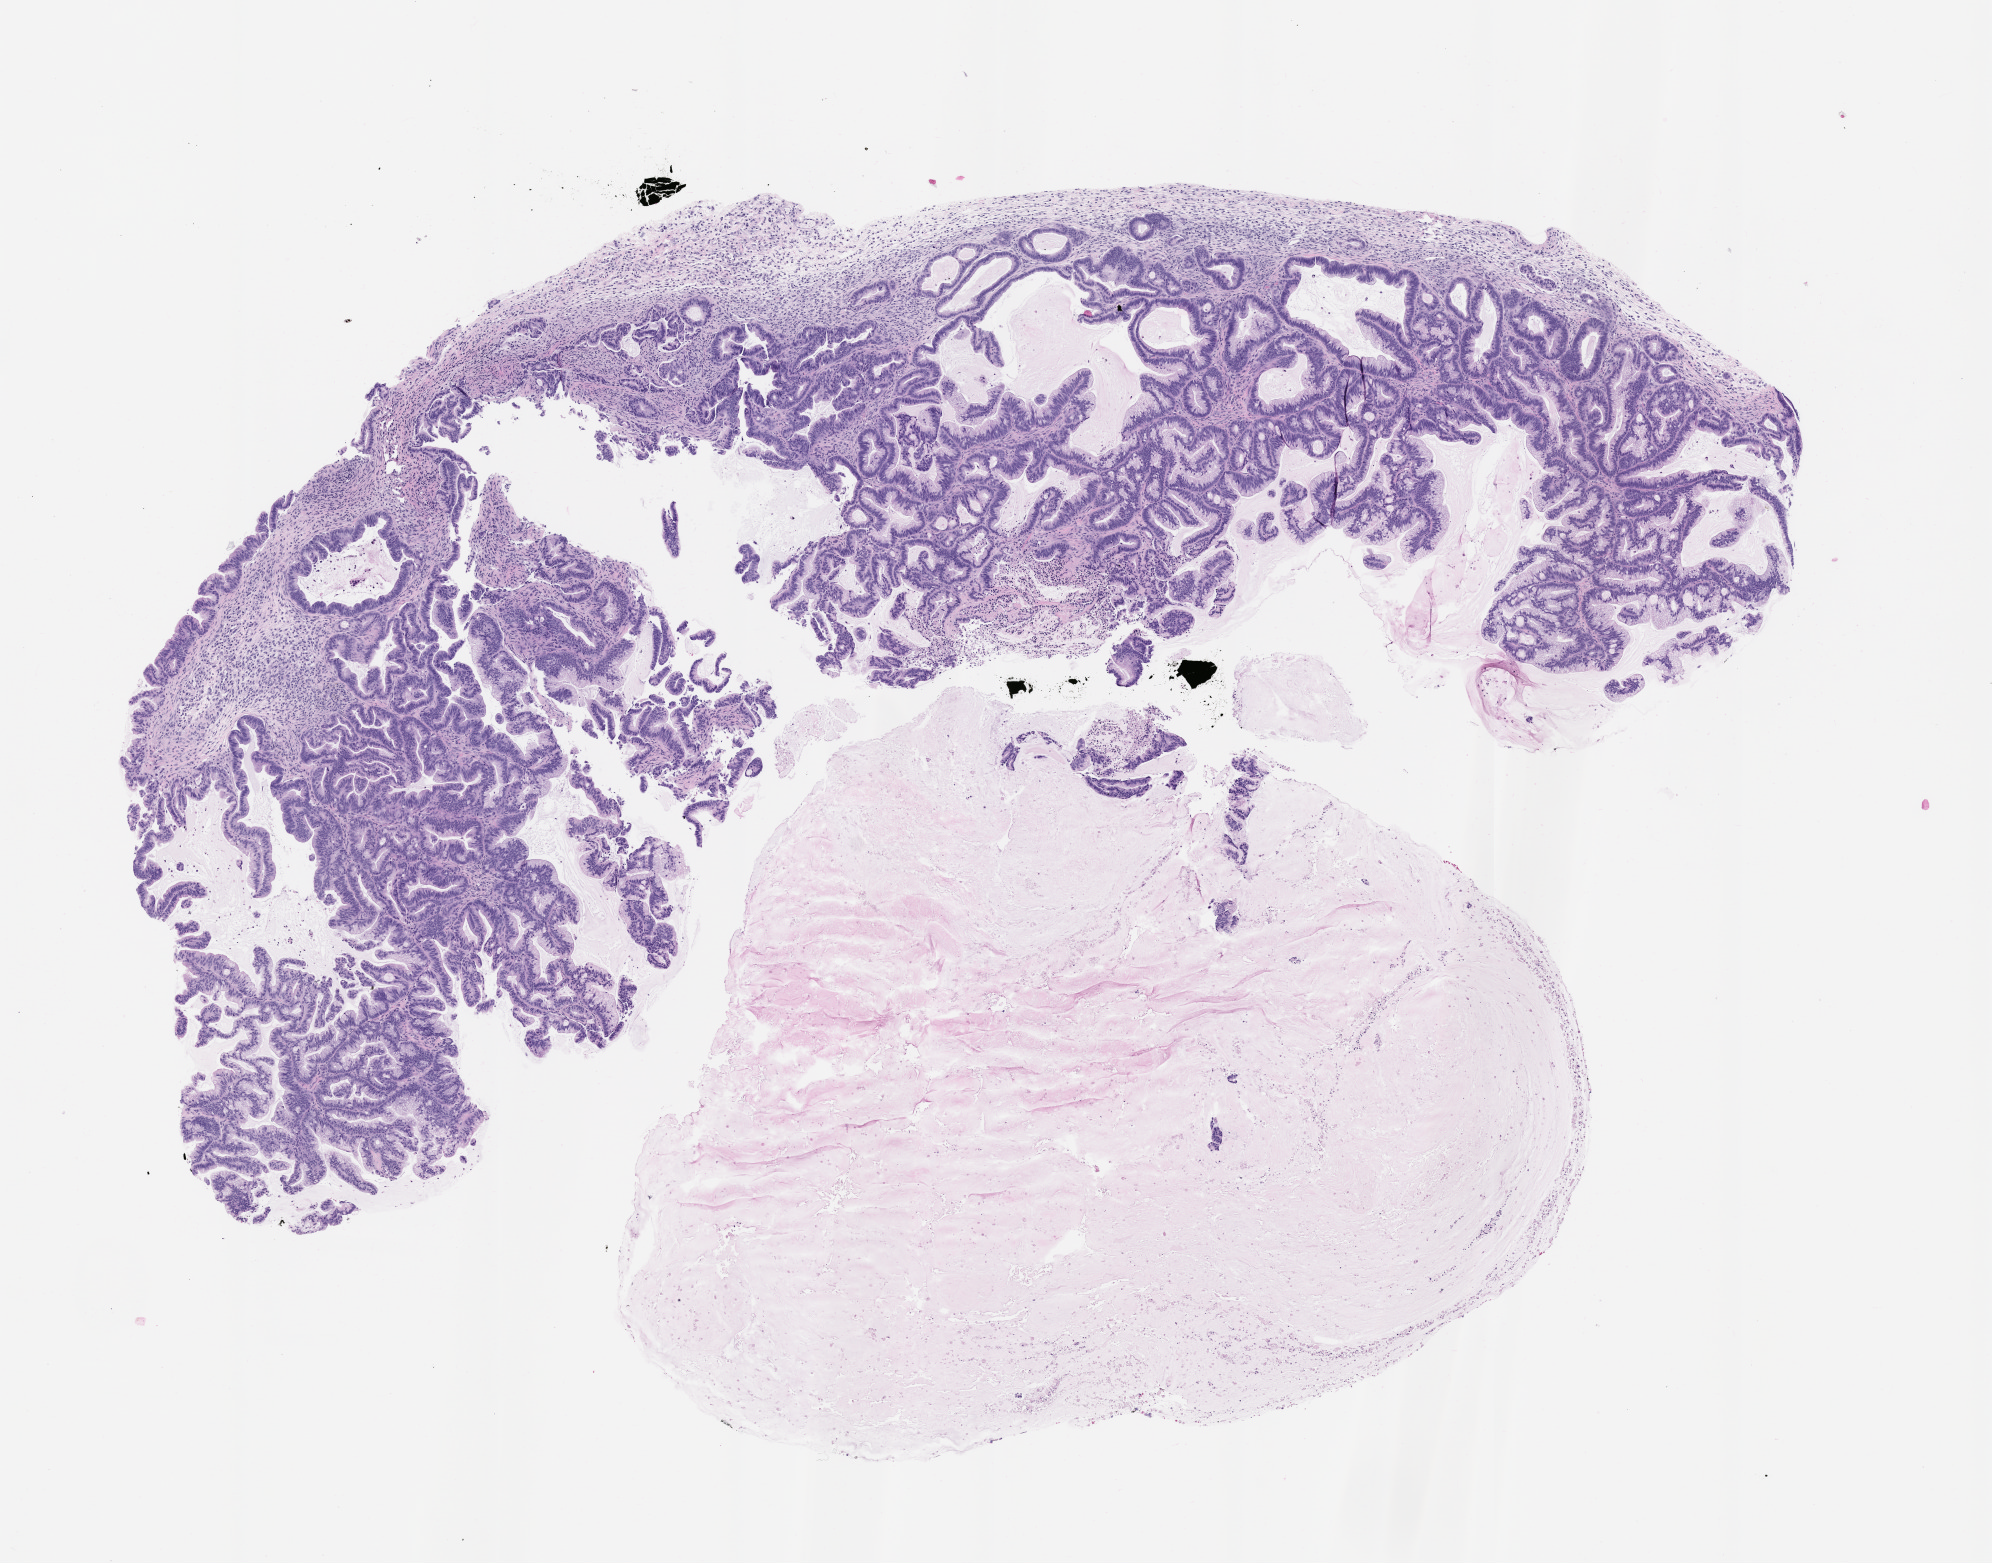
Whole-slide image, haematoxylin and eosin: patient-derived xenograft (human tumor grown in a mouse), passage 0, low-resolution overview of the scanned area, about 8.0 x 6.3 mm. FFPE section. Originating tumor site category: pancreas.
Originating patient diagnosis: Pancreatic Adenocarcinoma.